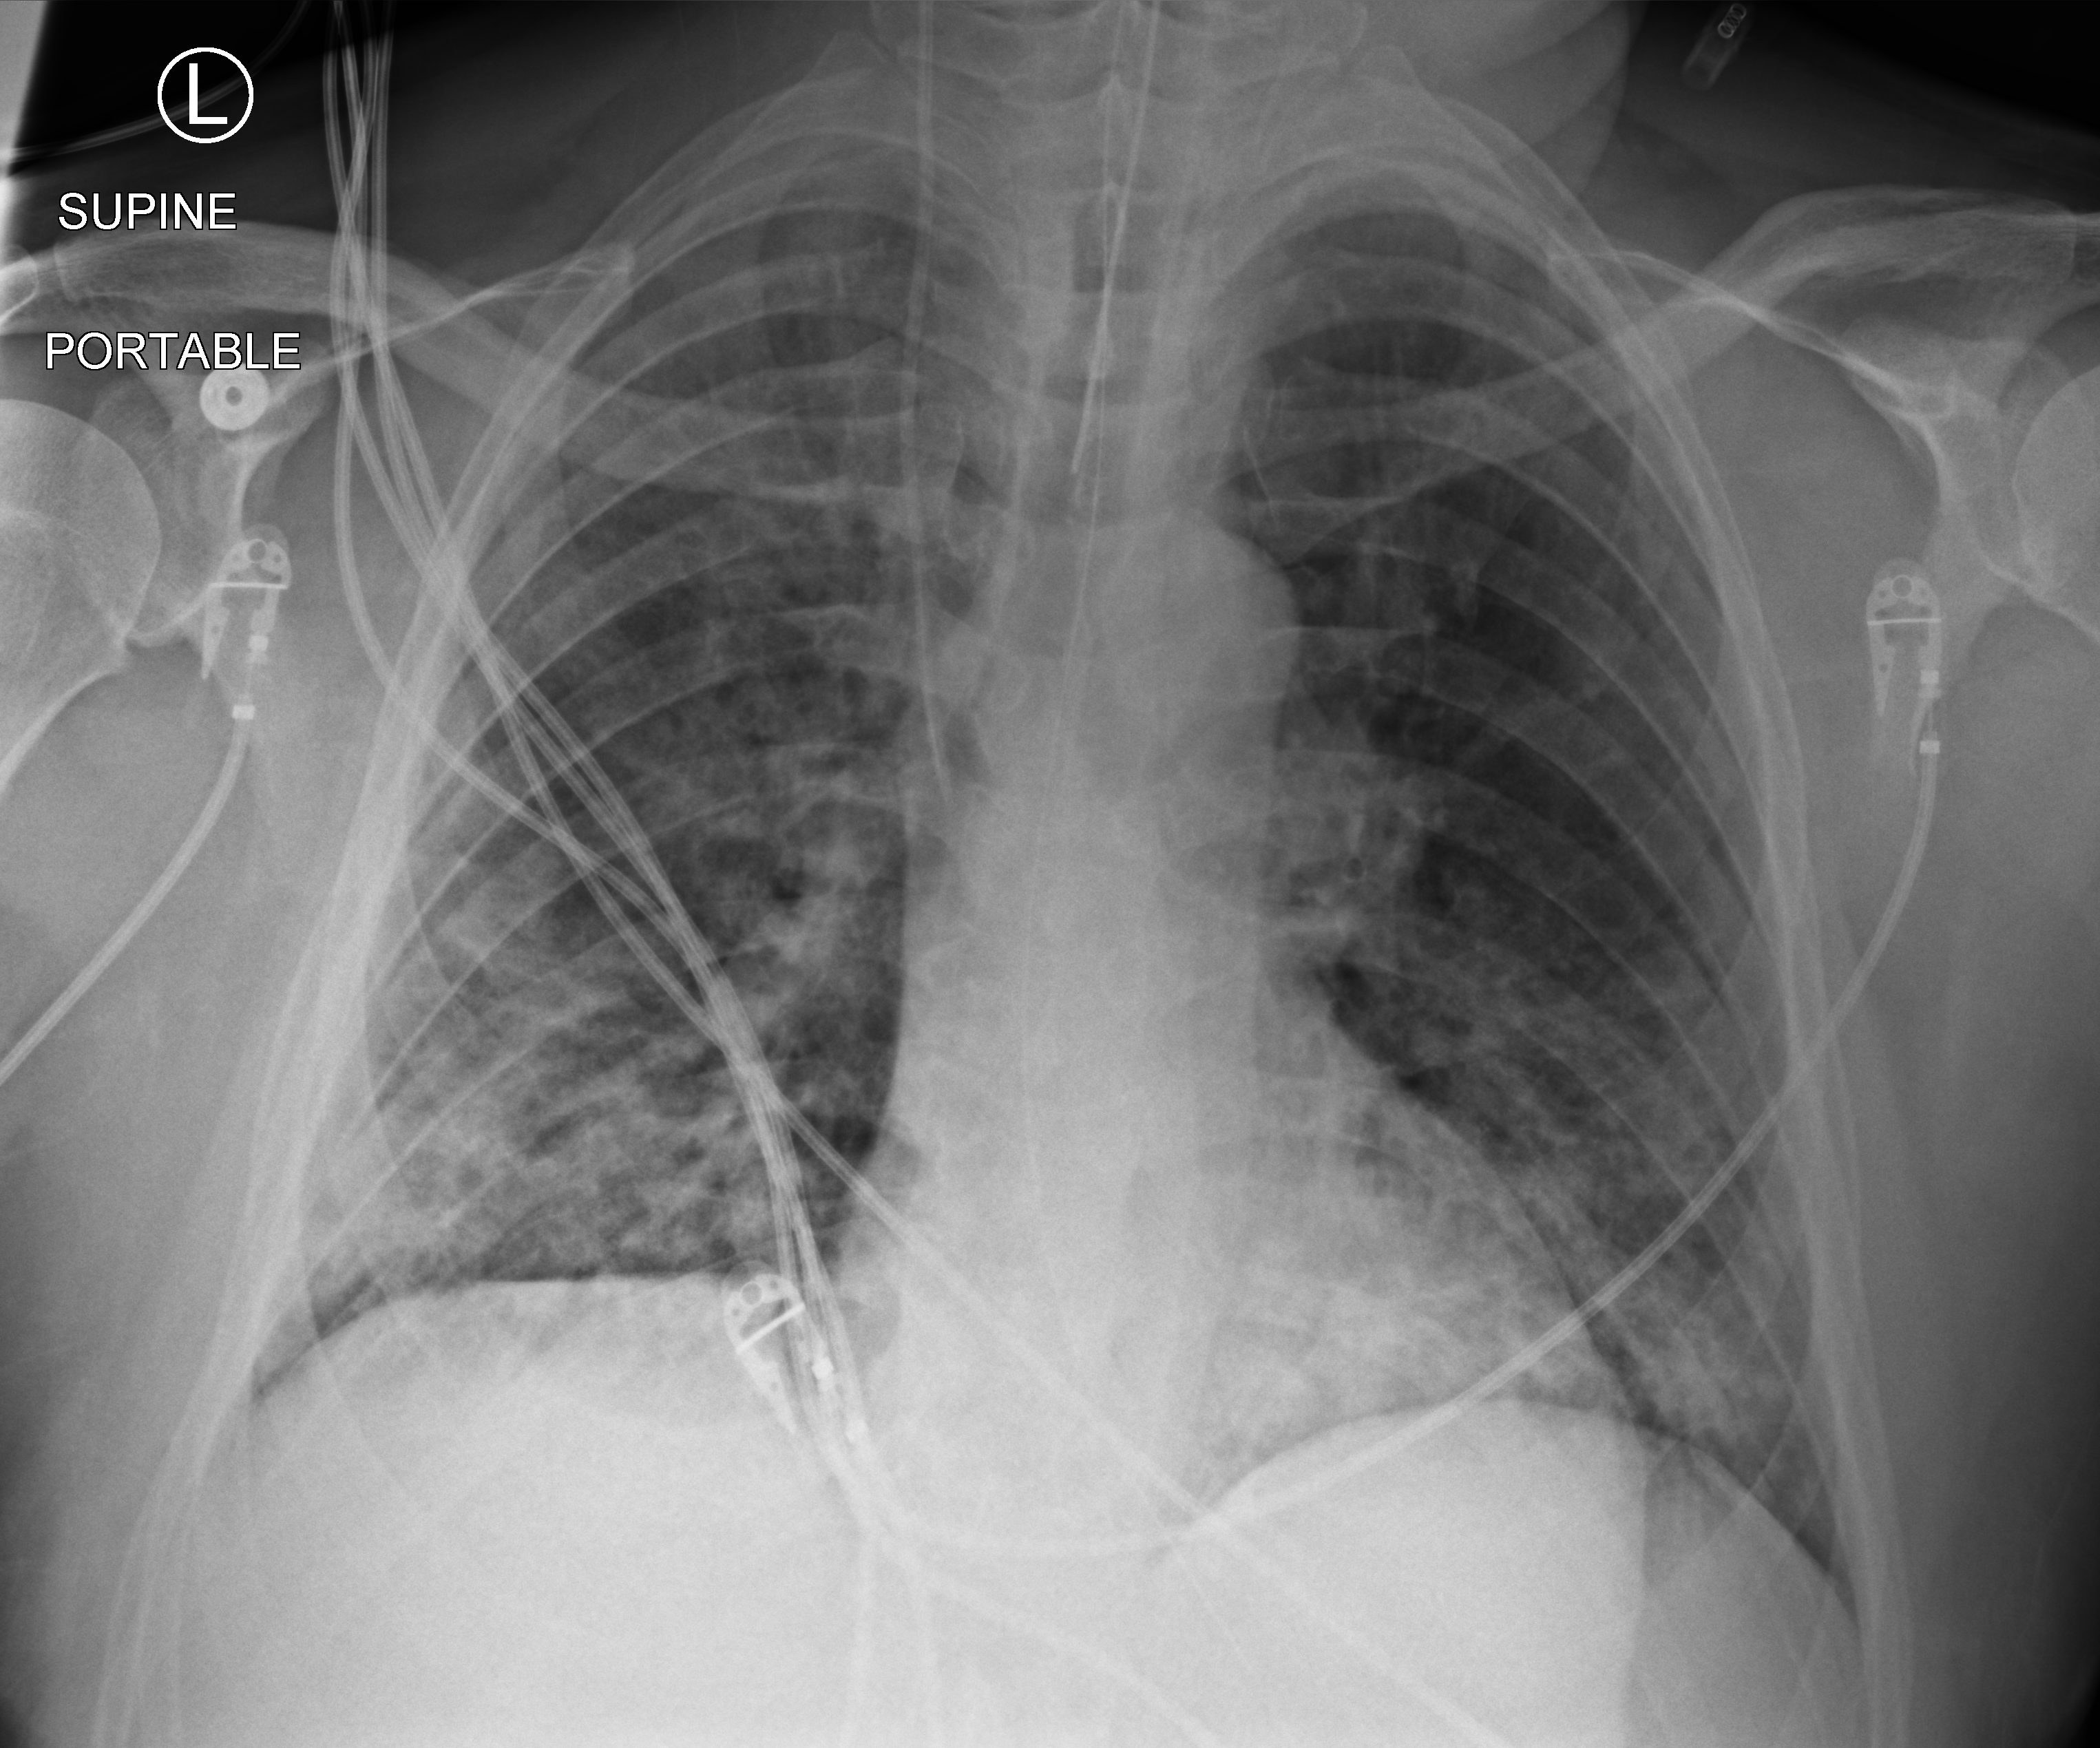
Portable chest radiograph; anteroposterior (AP) projection. Patient hospitalised with COVID-19; male, aged 18–59 years.
From the hospital-stay record, not from the radiograph (when in the stay this image was taken is not recorded): admitted to intensive care during this hospital stay: no.